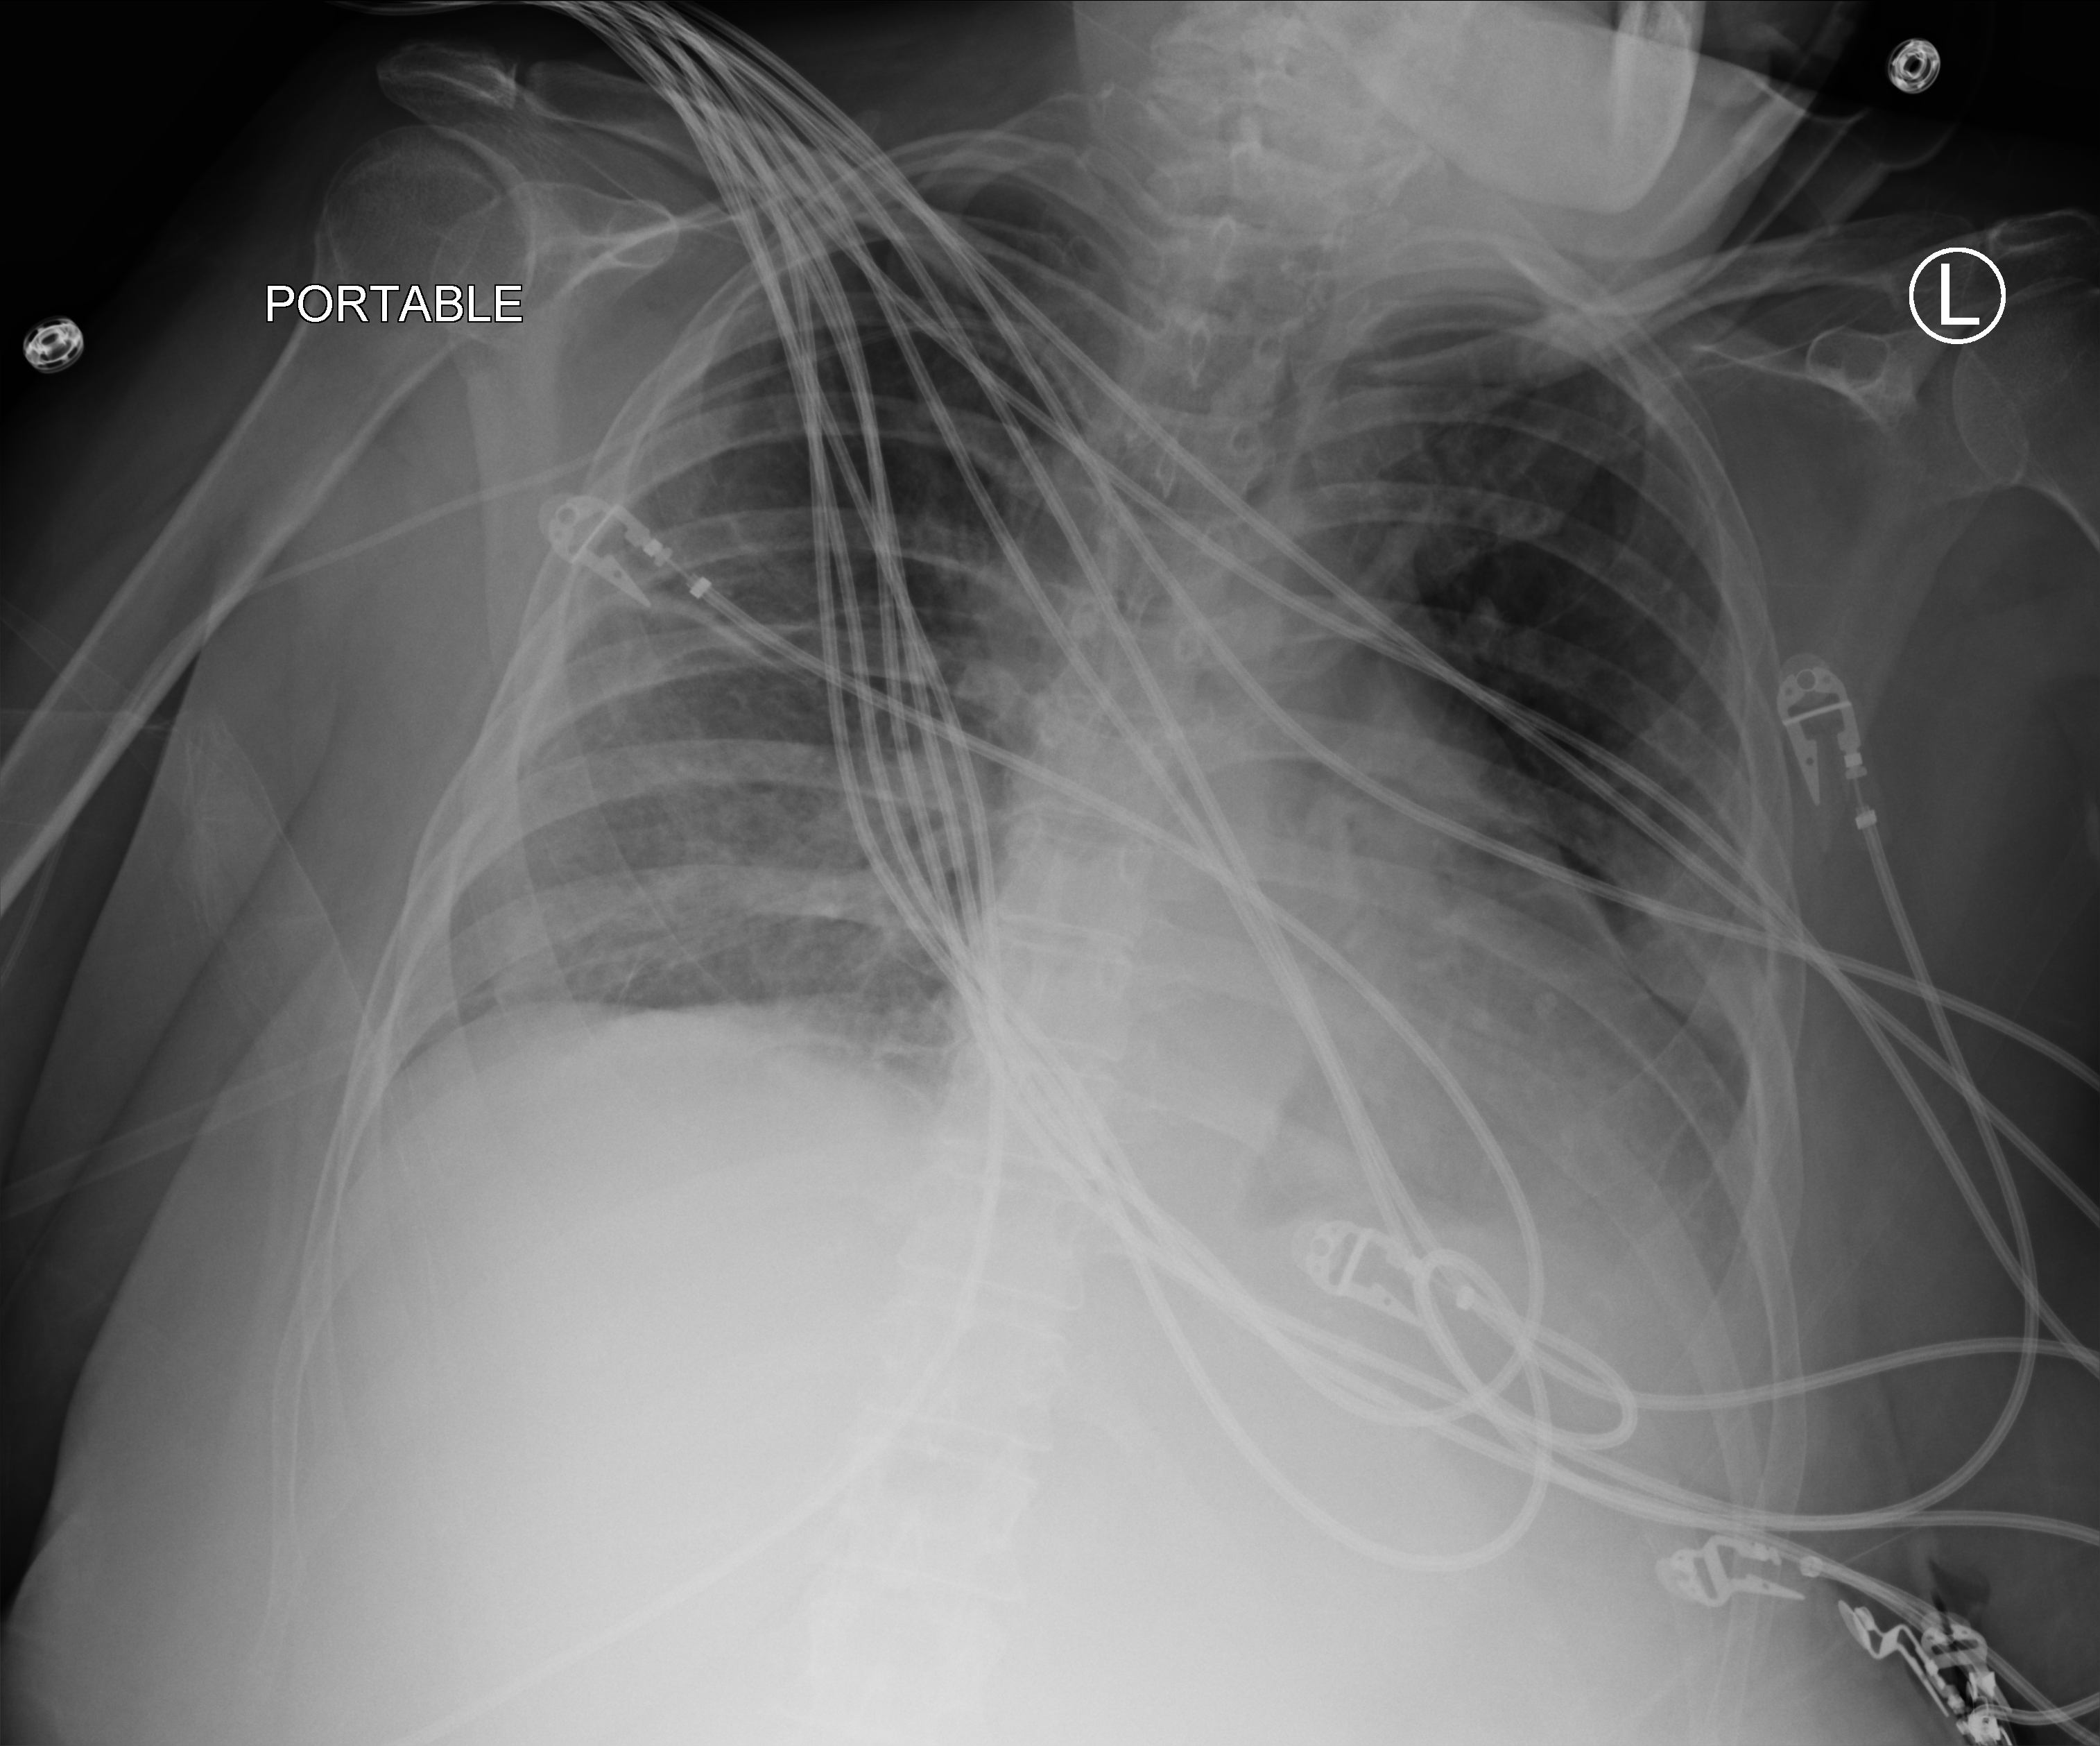
Bedside chest radiograph (computed radiography); anteroposterior (AP) projection. Patient hospitalised with COVID-19; female, aged 60–74 years.
From the hospital-stay record, not from the radiograph (when in the stay this image was taken is not recorded):
- admitted to intensive care during this hospital stay: yes